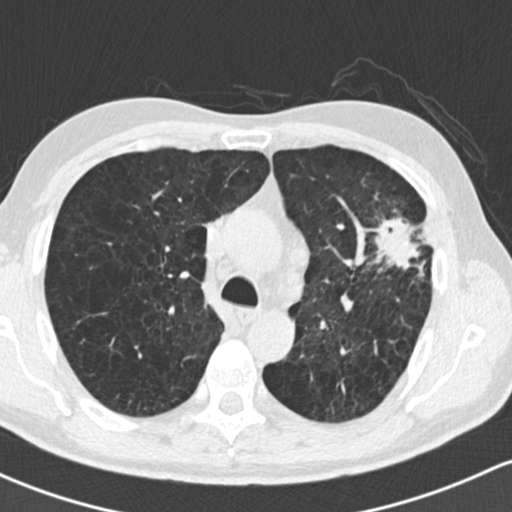
Chest CT (low-dose screening protocol), one axial image, baseline annual screen, lung window (W 1500 / L -600 HU), 2 mm slice thickness, standard (soft-tissue) reconstruction kernel (B30f), slice 56 of 162 in the series. Male participant, aged 61 years at enrolment. Former smoker at enrolment.
- Expert reader's lesion annotation, bounding box (x1, y1, x2, y2) in pixels: (354, 185, 449, 291).
- The exam's reader record, not a measurement of the box and not confirmed to be the same lesion: non-calcified nodule or mass ≥4 mm, left upper lobe, 35 × 35 mm, spiculated (stellate) margins, soft tissue attenuation.
- Later outcome: lung cancer diagnosed 19 days after this screen — adenocarcinoma, NOS, left upper lobe, well differentiated (G1), stage IIIA (AJCC 6th edition), 45 mm at pathology.